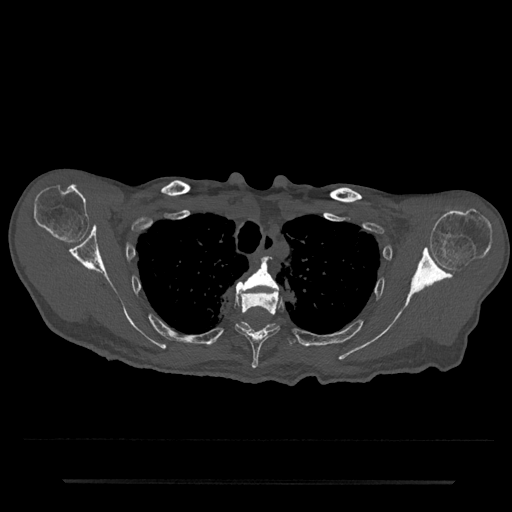
CT including the spine, one axial slice. Position 620 of 797 along the scan axis. Reconstruction kernel Br40s/3. Bone window (W 1800 / L 400 HU). 0.5 mm slice thickness. 512 × 512 image matrix, field of view 427 × 427 mm. Male patient, age 74 years. Case-level facts recorded for this patient, not image findings: primary cancer: prostate.
Annotated regions visible in this slice (semi-automatically segmented with operator editing):
- T3 vertebra: bounding box <236,263,279,293> (left, top, right, bottom; pixels)
- T4 vertebra: <235,290,281,369>
- T5 vertebra: <218,322,296,346>